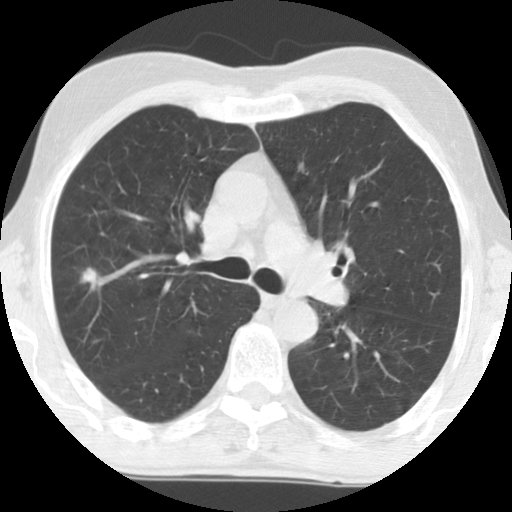
Low-dose screening chest CT, axial slice; baseline annual screen; lung window (W 1500 / L -600 HU); 2.5 mm slice thickness; slice 46 of 133 in the series; 512 × 512 image matrix. Male participant, aged 69 years at enrolment. Former smoker at enrolment.
Expert reader's lesion annotation, bounding box <57,254,119,312> (left, top, right, bottom; pixels). Reader record for this screening exam (exam-level; its link to the box is not recorded): non-calcified nodule or mass ≥4 mm, right upper lobe, 8 × 8 mm, spiculated (stellate) margins, soft tissue attenuation. Later outcome: lung cancer diagnosed 588 days after this screen — mucinous adenocarcinoma, right upper lobe, moderately differentiated (G2), stage IA (AJCC 6th edition), 11 mm at pathology.